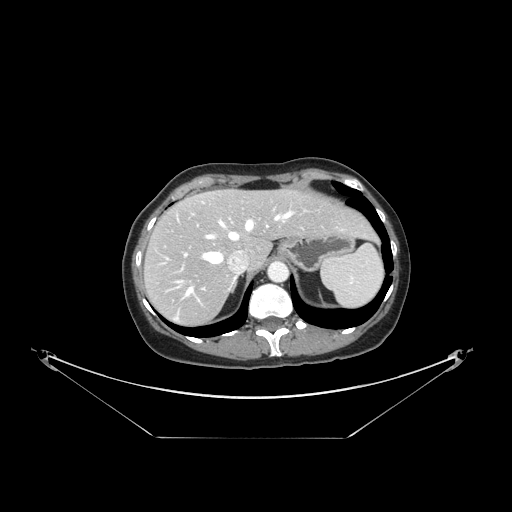
Contrast-enhanced abdominal CT, one axial slice. Slice 116 of 148 in the series (ordered by position). Intravenous contrast given. Soft-tissue window (W 400 / L 40 HU). 2.5 mm slice thickness. 512 × 512 image matrix, field of view 500 × 500 mm. Female patient, age 73 years. Case-level facts recorded for this patient, not image findings: diagnosis: colorectal cancer liver metastases, imaged before liver resection; multiple liver metastases: no; largest metastasis: 1 cm; chemotherapy before resection: yes.
Outlined on this slice (outlined manually by an expert reader):
- hepatic veins: bounding box <186,210,294,296> (left, top, right, bottom; pixels)
- liver: <146,190,373,324>
- planned liver remnant (the part of the liver to remain after resection): <170,191,373,266>
- portal vein (with intrahepatic branches): <184,218,230,290>